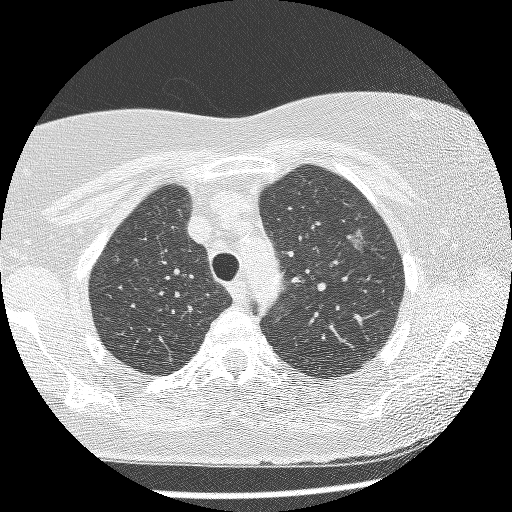
Axial slice from a low-dose chest CT screening exam, first (baseline) screen, lung window (W 1500 / L -600 HU), lung (sharp) reconstruction kernel (BONE), 120 kVp, slice 181 of 241 in the series. Female, age 61 years at enrolment.
Expert-annotated lung lesion, box from (x=329, y=219) to (x=382, y=267) px. The screening reader recorded 4 non-calcified nodules or masses ≥4 mm on this exam; which of them this box marks is not recorded. Official screen result: positive, change unspecified: nodule(s) >= 4 mm or enlarging nodule(s), mass(es), or other non-specific abnormalities suspicious for lung cancer. Lung cancer was diagnosed 111 days after this screen: bronchiolo-alveolar adenocarcinoma, NOS, left upper lobe, stage IV (AJCC 6th edition), 10 mm at pathology.